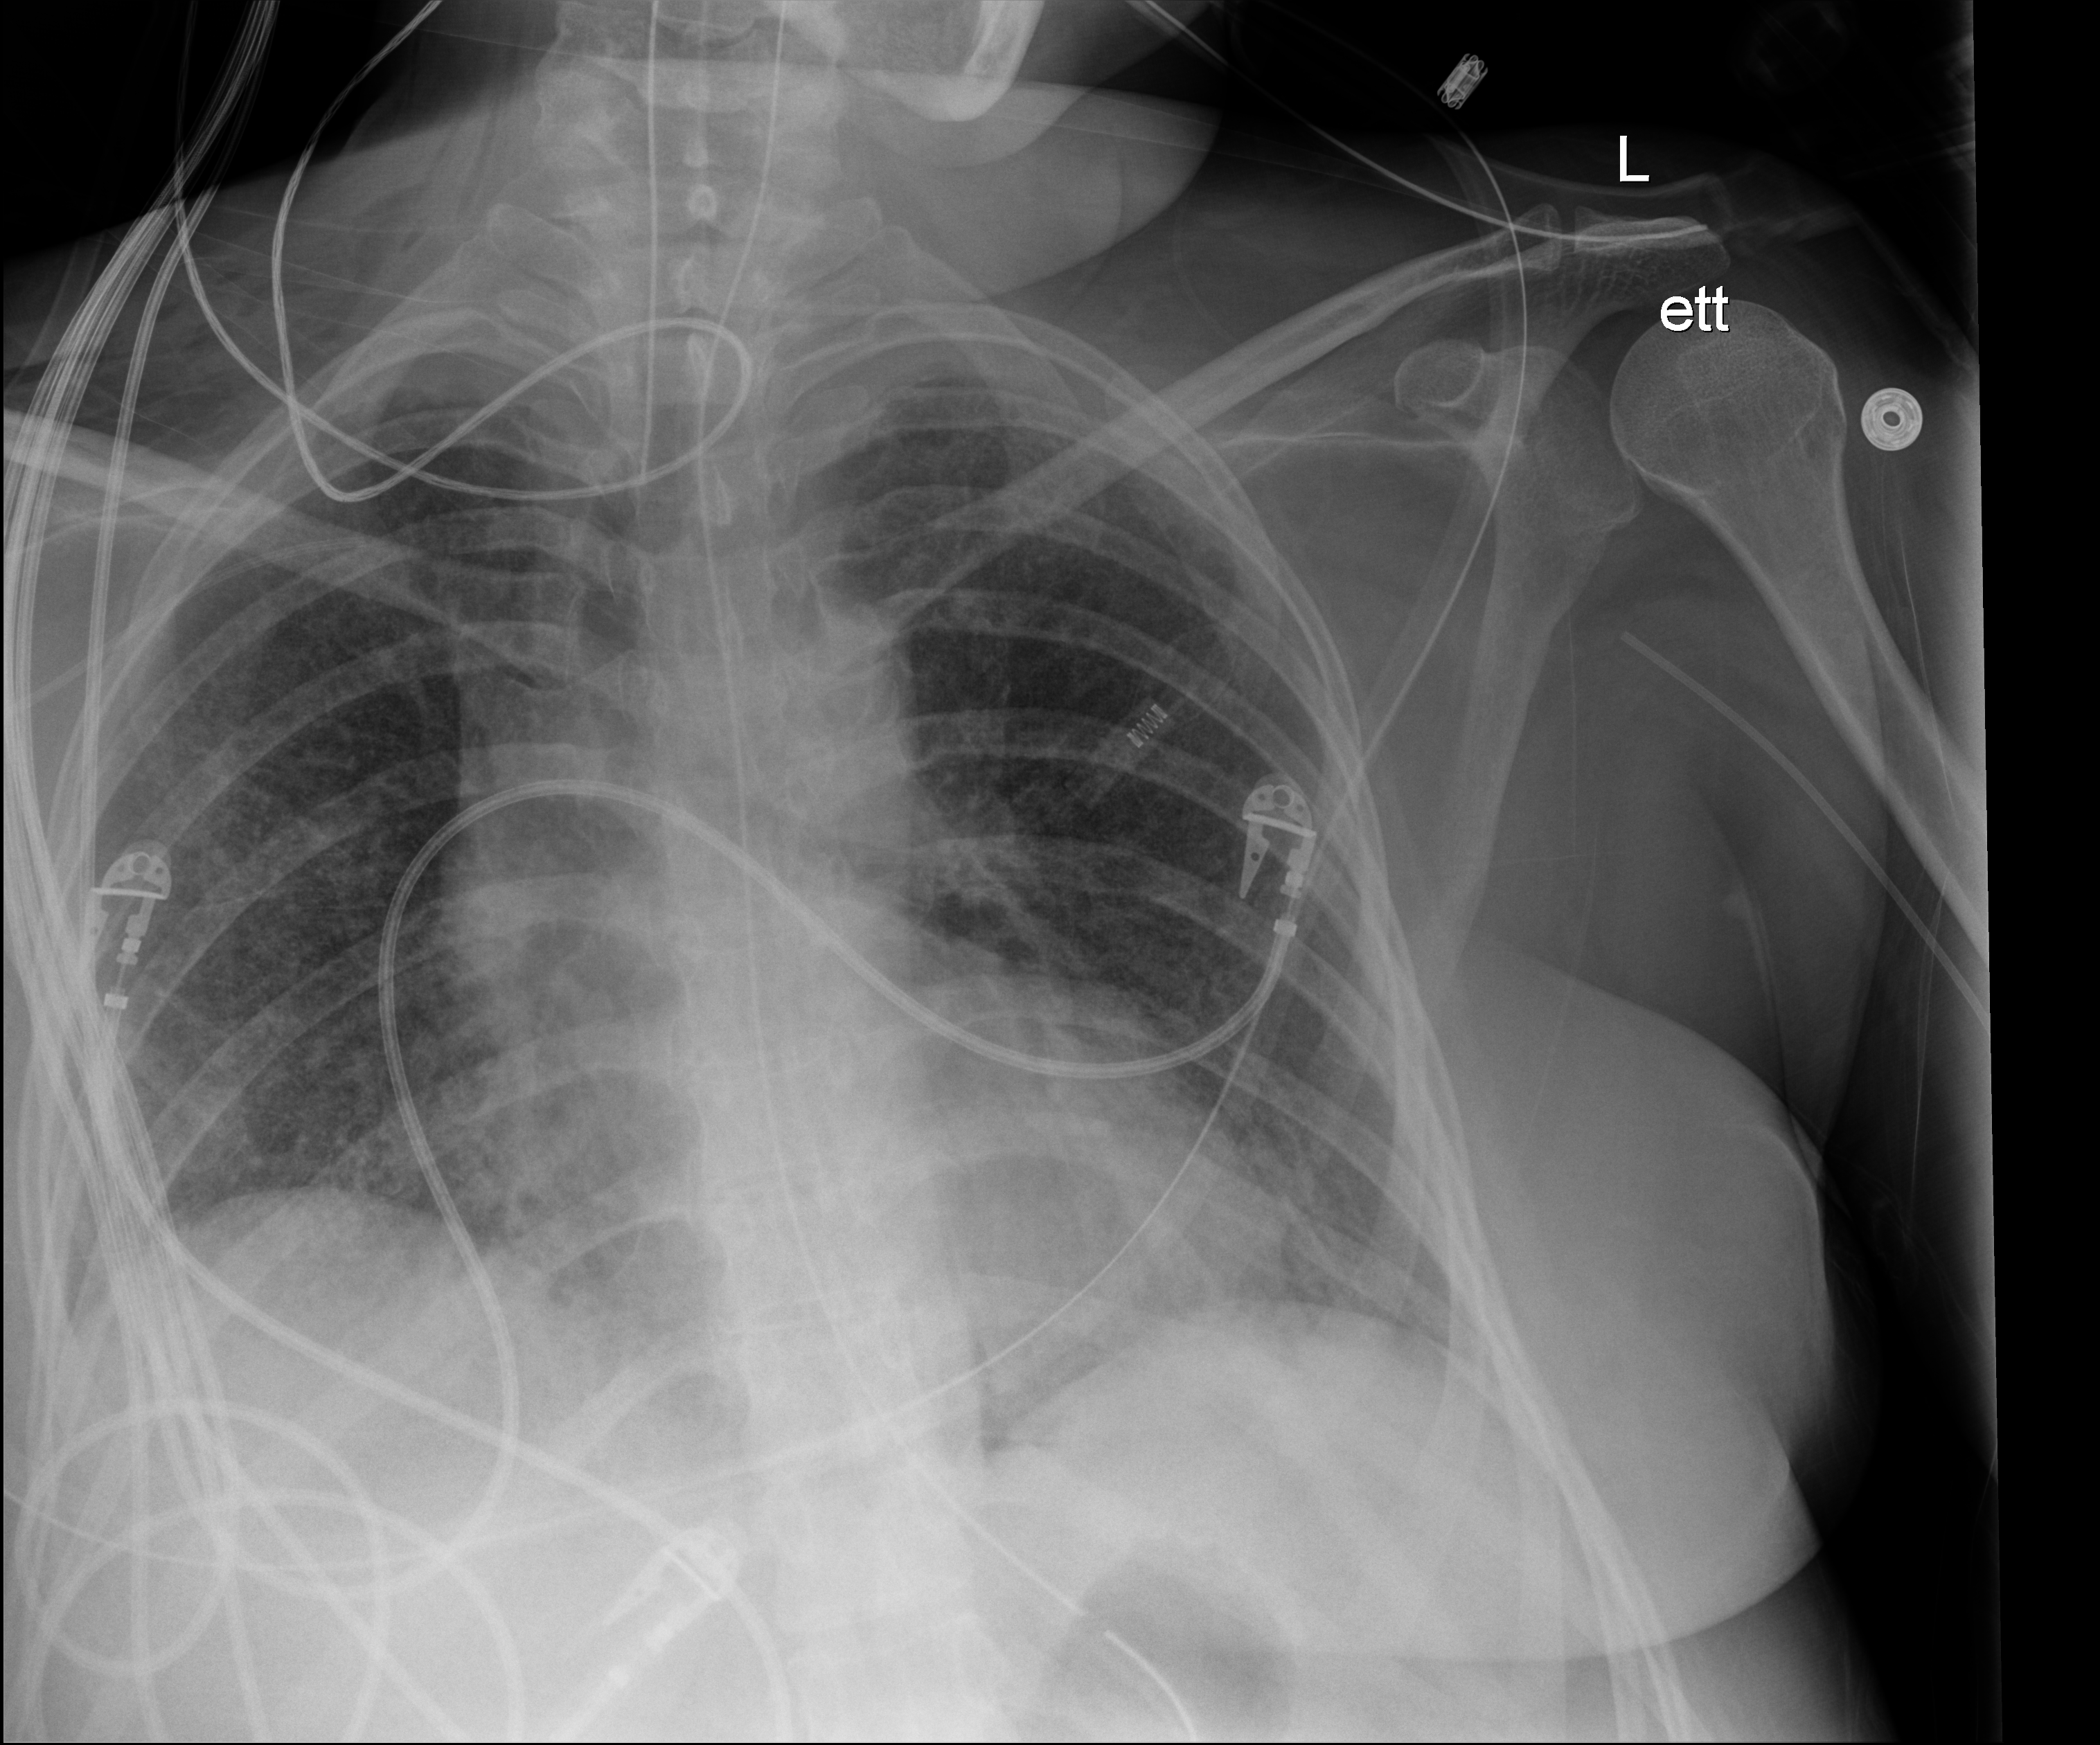
Chest radiograph (digital radiography); anteroposterior (AP) projection. Female patient hospitalised with COVID-19, age 18–59 years.
Hospital-stay facts (about this admission, not read from this image; timing relative to this image not recorded):
- length of hospital stay: 73 days